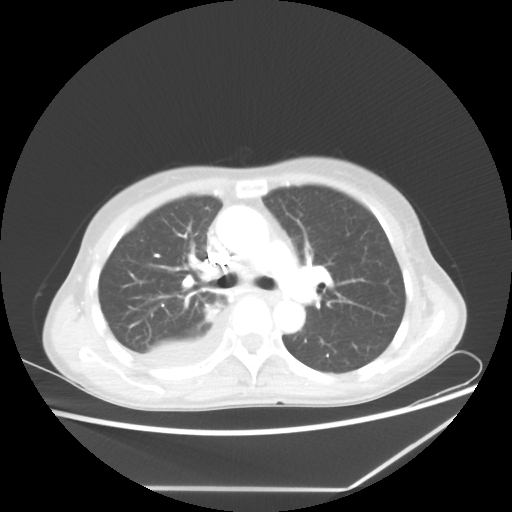
Chest CT, one axial slice; position 38 of 60 along the scan axis; 80 kVp; lung window (W 1500 / L -600 HU); 512 × 512 image matrix, field of view 364 × 364 mm. Female patient, age 59 years. From the clinical record (not read from this slice): clinical TNM (as recorded): T1c N1 M1.
Annotated regions visible in this slice (bounding box drawn by a radiologist):
- lung tumour (recorded histology: adenocarcinoma): box from (x=201, y=301) to (x=222, y=324) px